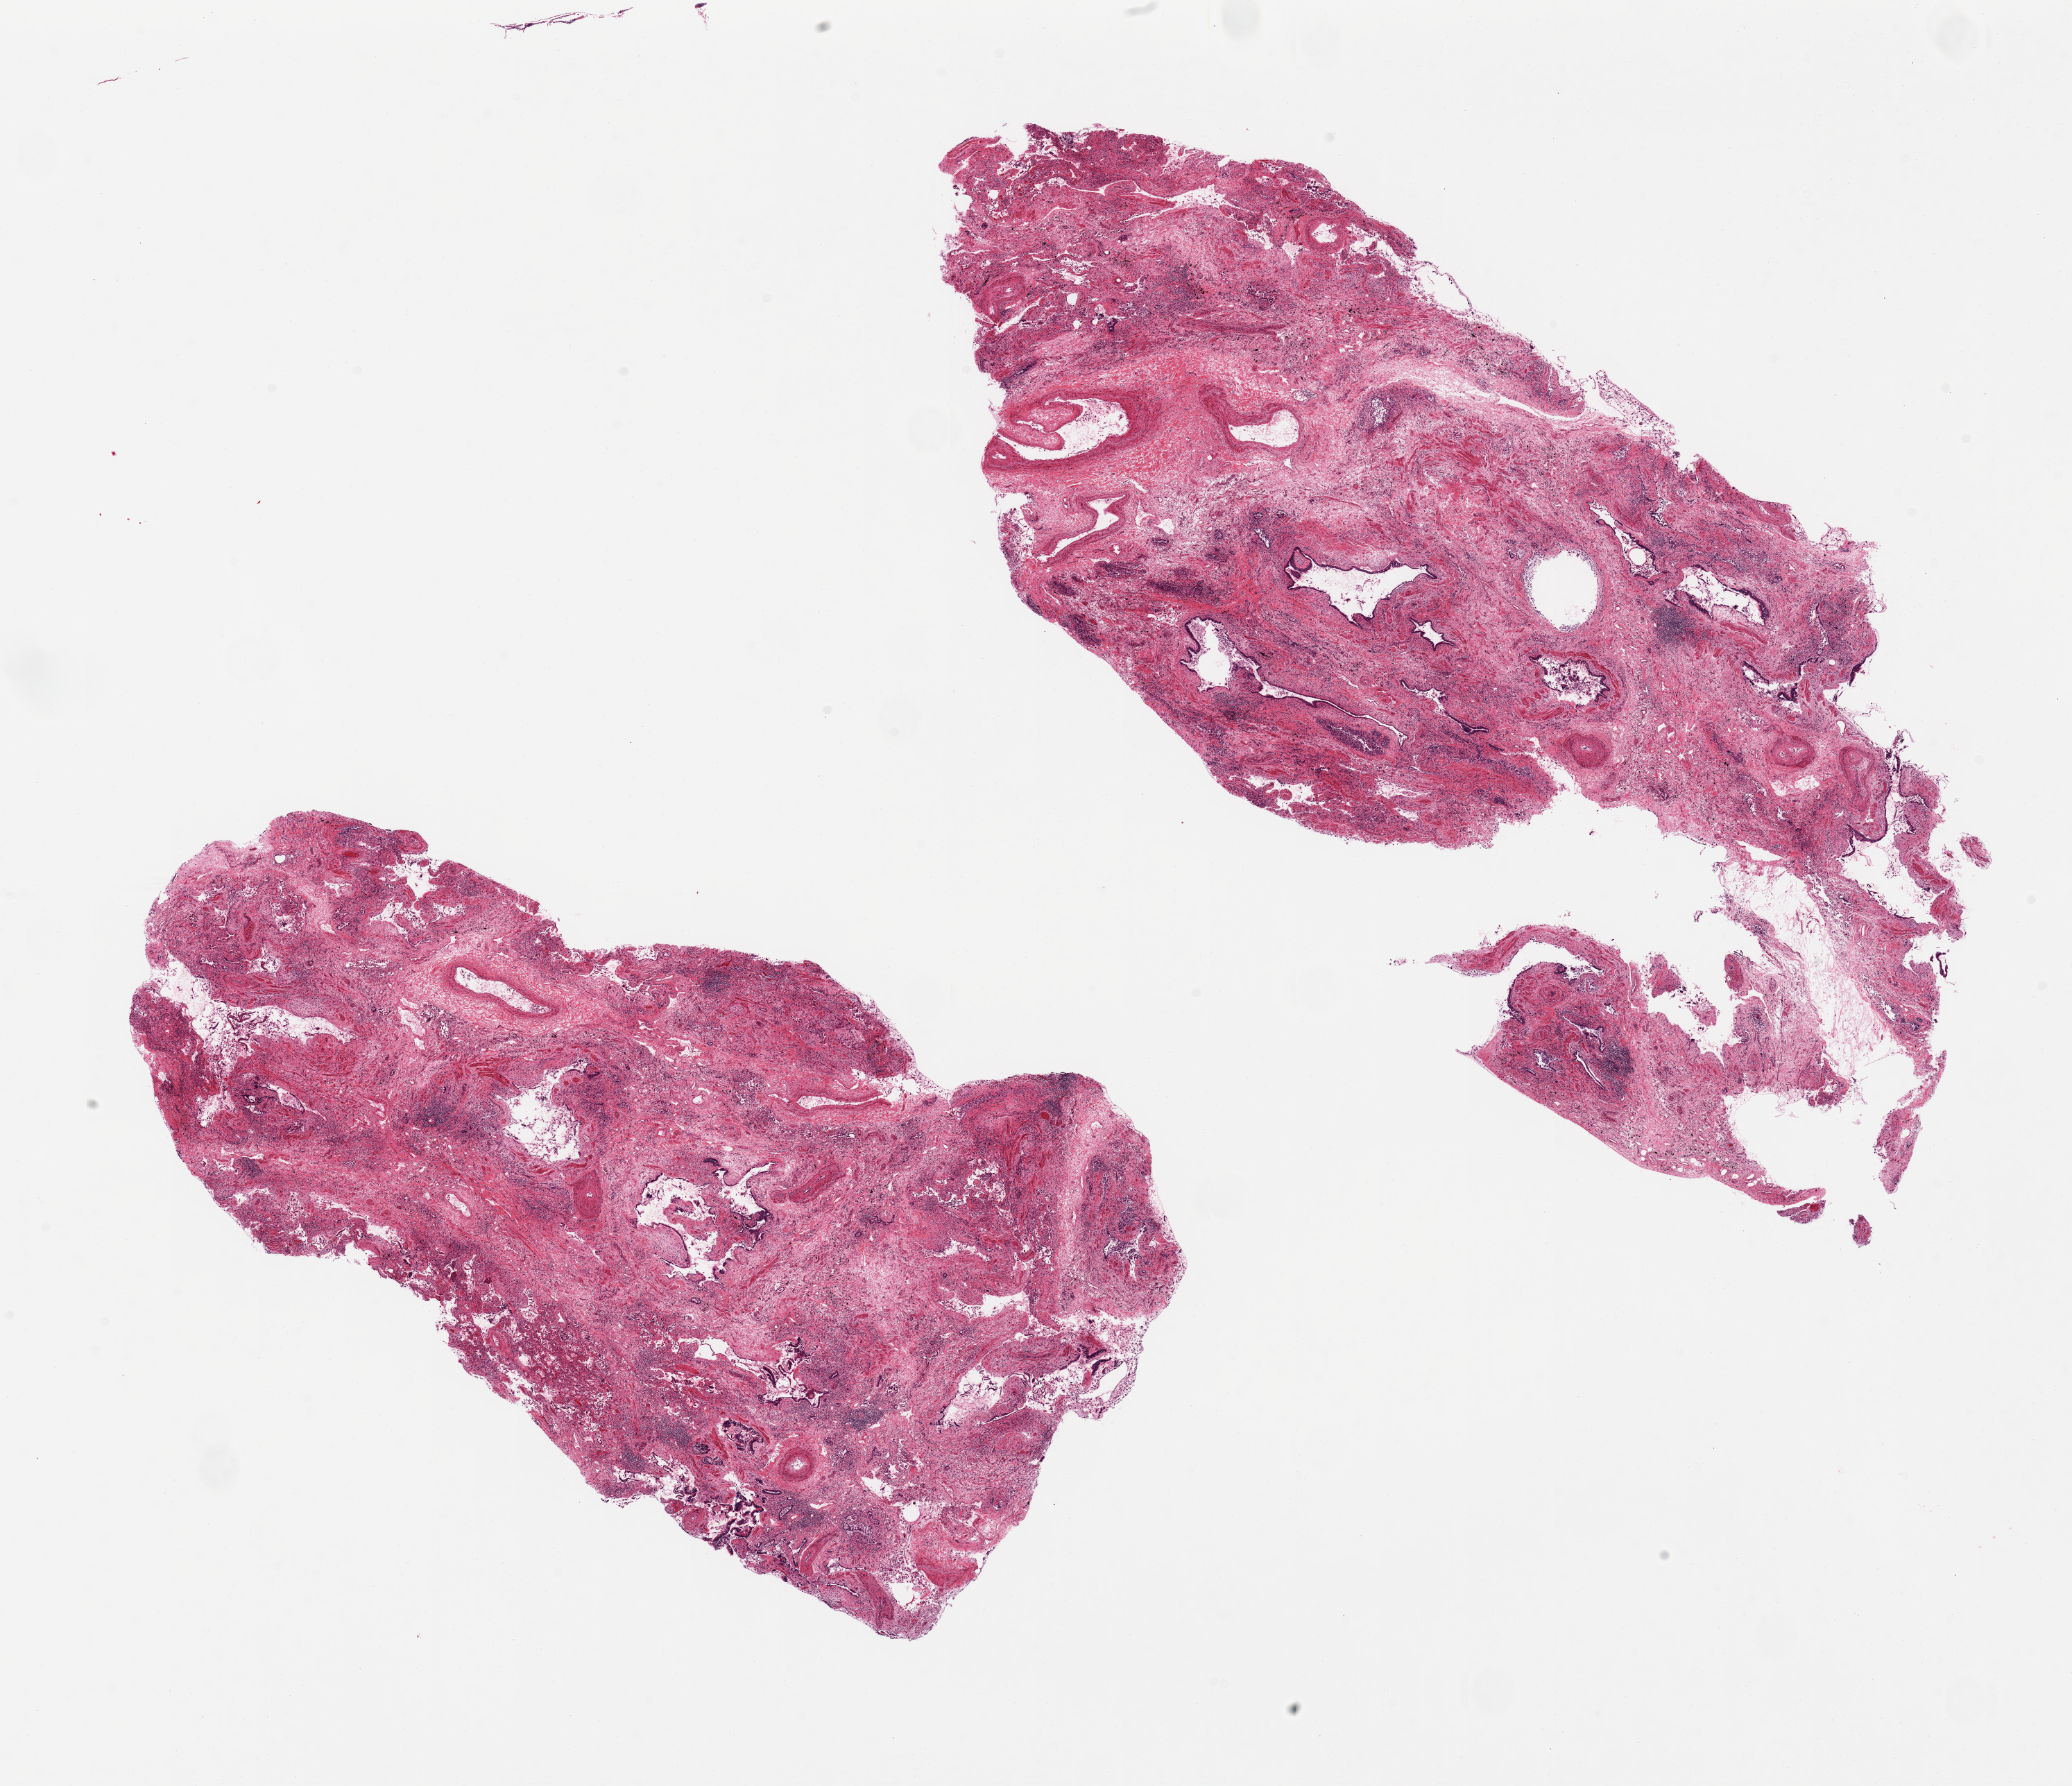
Whole-slide image, hematoxylin and eosin (H&E) stain — whole scanned area (about 23.6 x 20.4 mm) shown as a low-resolution overview, PAXgene-fixed paraffin-embedded (PFPE) section, sampled site (target tissue): lung, tissue donor sample.
Pathologist's review note for this sample: 2 pieces; severe fibrosis, vascular thickening and bronchiectasis with no normal parenchyma.